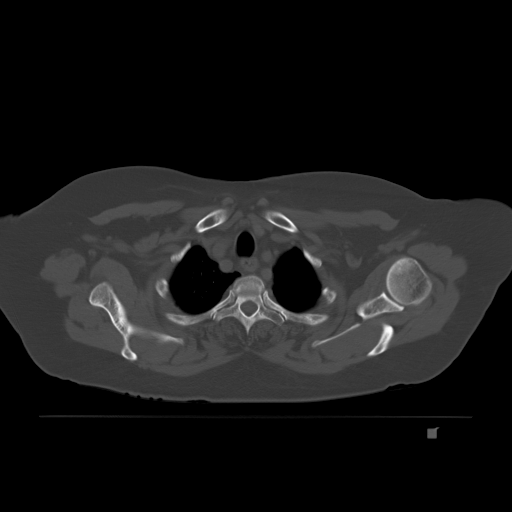
CT including the spine, one axial slice; slice 168 of 221 in the series (ordered by position); bone window (W 1800 / L 400 HU); 3 mm slice thickness; 512 × 512 image matrix, field of view 474 × 474 mm. Female patient, age 63 years. From the clinical record (not read from this slice): primary cancer: breast.
Outlined on this slice (semi-automatic segmentation, software-assisted and operator-edited):
- T3 vertebra: bounding box [x1, y1, x2, y2] px = [236, 315, 283, 322]